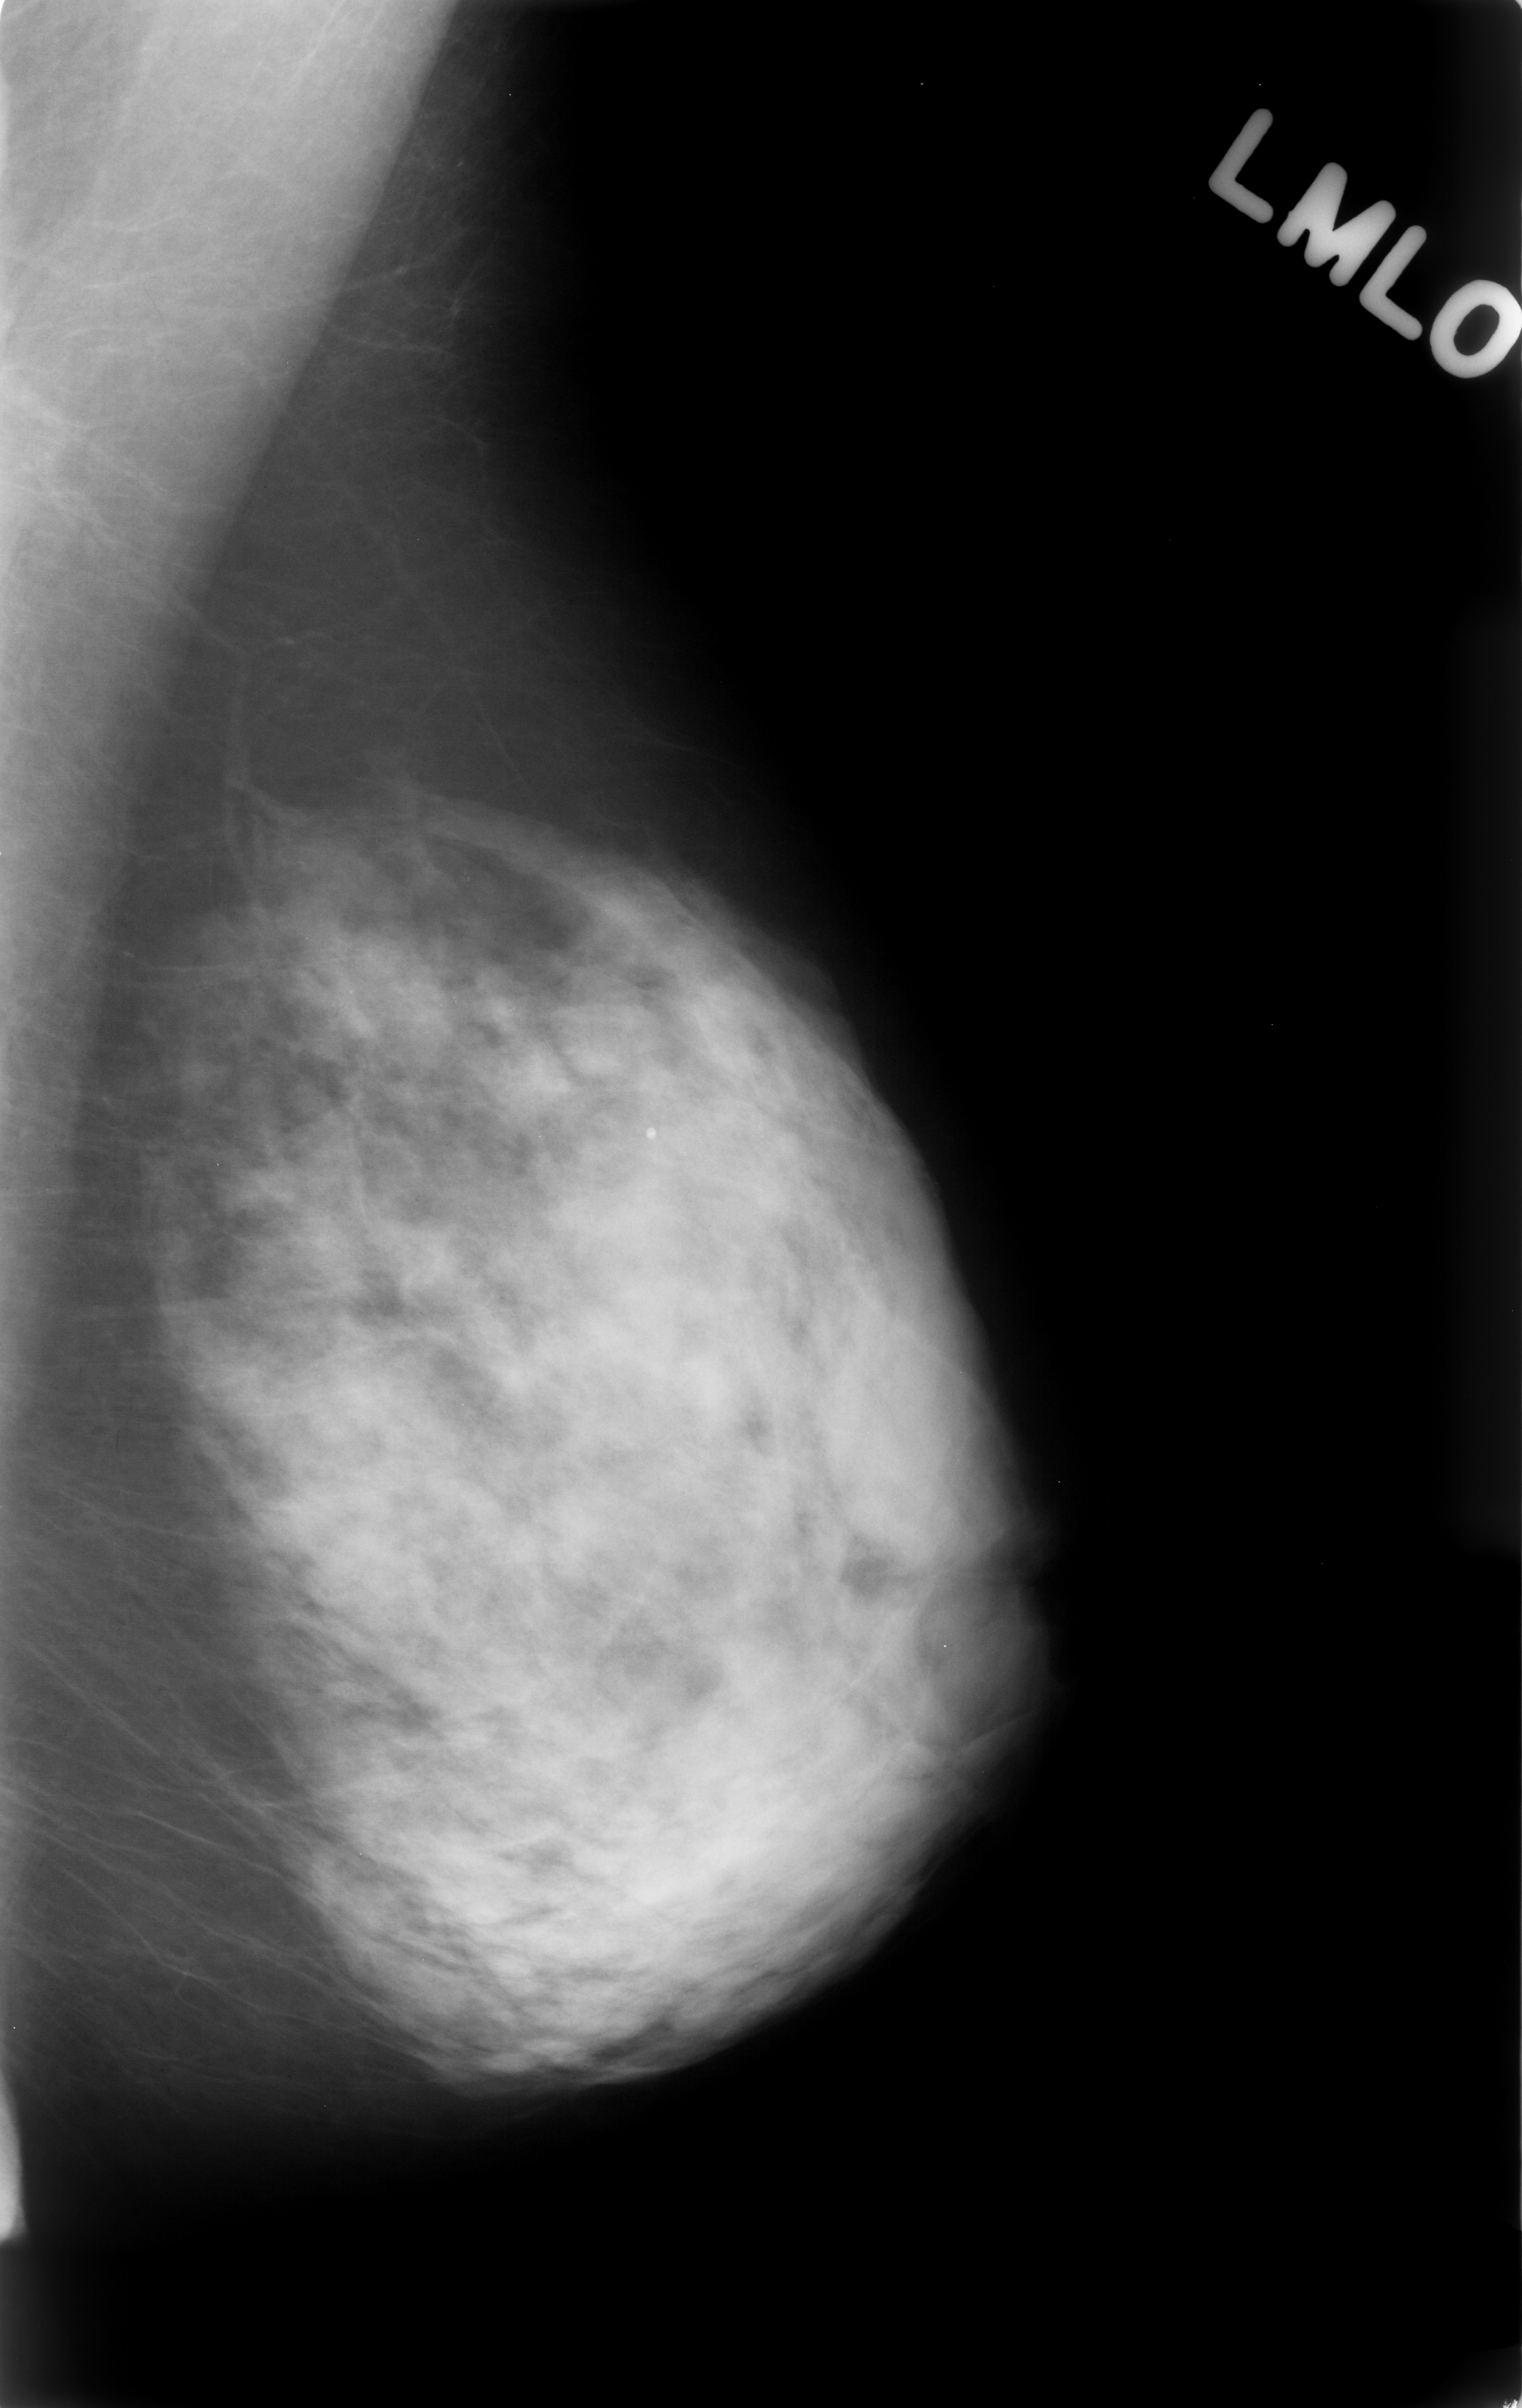
Digitized screen-film mammogram; left breast; MLO view; BI-RADS breast density category 4 (scale 1–4); 1522 × 2408 image matrix.
Expert-marked regions of interest on this image (one box per marked abnormality):
- calcifications, morphology amorphous, distribution segmental; BI-RADS assessment category 4; pathology result (as recorded, not read from the image): benign: box from (x=248, y=872) to (x=650, y=1152) px